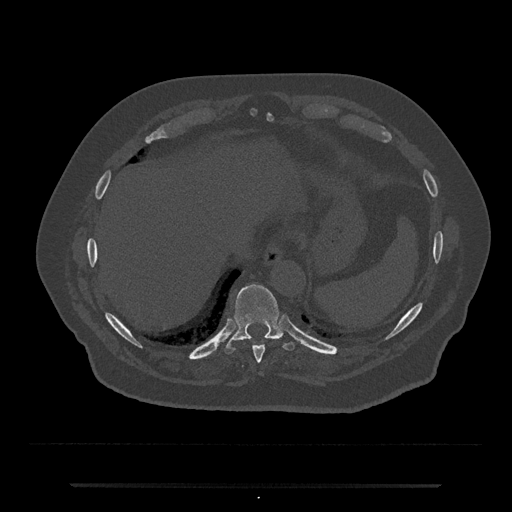
CT including the spine, one axial slice. Slice 726 of 797 in the series (ordered by position). Reconstruction kernel Br40s/3. 120 kVp. Bone window (W 1800 / L 400 HU). 0.5 mm slice thickness. 512 × 512 image matrix, field of view 434 × 434 mm. Patient: male, 80 years. From the clinical record (not read from this slice): primary cancer: prostate.
Outlined on this slice (semi-automatically segmented with operator editing):
- T10 vertebra: bounding box <224,284,295,354> (left, top, right, bottom; pixels)
- T9 vertebra: <253,345,265,364>